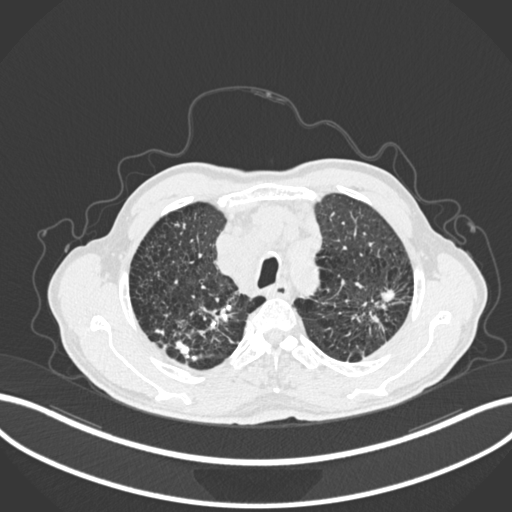
Chest CT, one axial slice; slice 225 of 287 in the series (ordered by position); reconstruction kernel B30f; 120 kVp; lung window (W 1500 / L -600 HU); 512 × 512 image matrix, field of view 400 × 400 mm. Male patient, age 74 years. Case-level facts recorded for this patient, not image findings: clinical TNM (as recorded): T2a N1 M0.
Annotated regions visible in this slice (bounding box drawn by a radiologist):
- lung tumour (recorded histology: adenocarcinoma): bounding box [x1, y1, x2, y2] px = [357, 286, 399, 329]